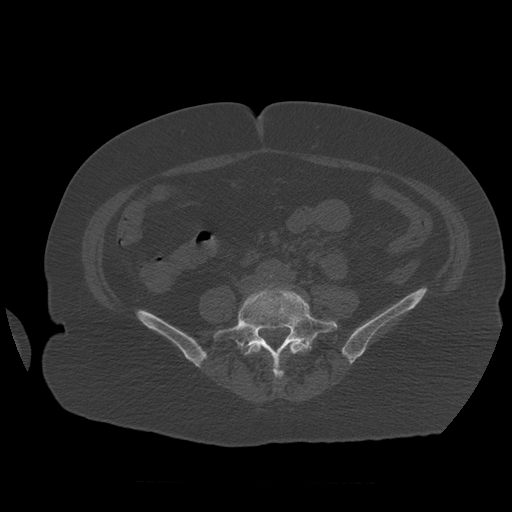
CT including the spine, one axial slice; reconstruction kernel STANDARD; bone window (W 1800 / L 400 HU); 1.25 mm slice thickness; 512 × 512 image matrix. Patient age 81 years. From the clinical record (not read from this slice): primary cancer: renal; vertebrae with lytic lesions (as recorded): L1.
Structures marked on this image (semi-automatically segmented with operator editing):
- L4 vertebra: box from (x=245, y=338) to (x=309, y=381) px
- L5 vertebra: (x=214, y=286)–(x=338, y=361)